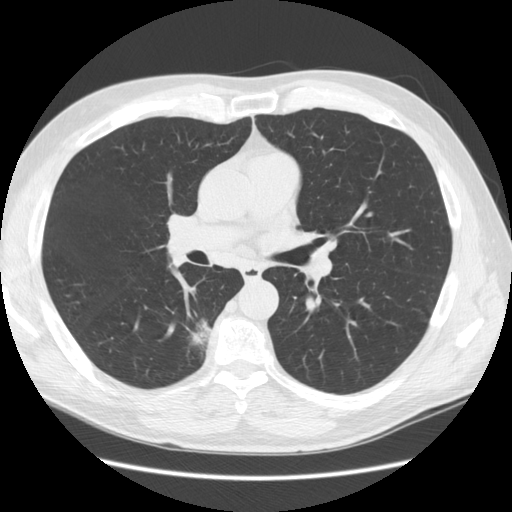
Low-dose screening chest CT, one axial slice. Slice 74 of 133 in the series (ordered by position). Reconstruction kernel STANDARD. 120 kVp. Lung window (W 1500 / L -600 HU). 2.5 mm slice thickness. 512 × 512 image matrix, field of view 370 × 370 mm.
Structures marked on this image (manually delineated by an expert):
- lesion 1 (tumor, lower lobe of right lung): bounding box [x1, y1, x2, y2] px = [190, 317, 211, 345]